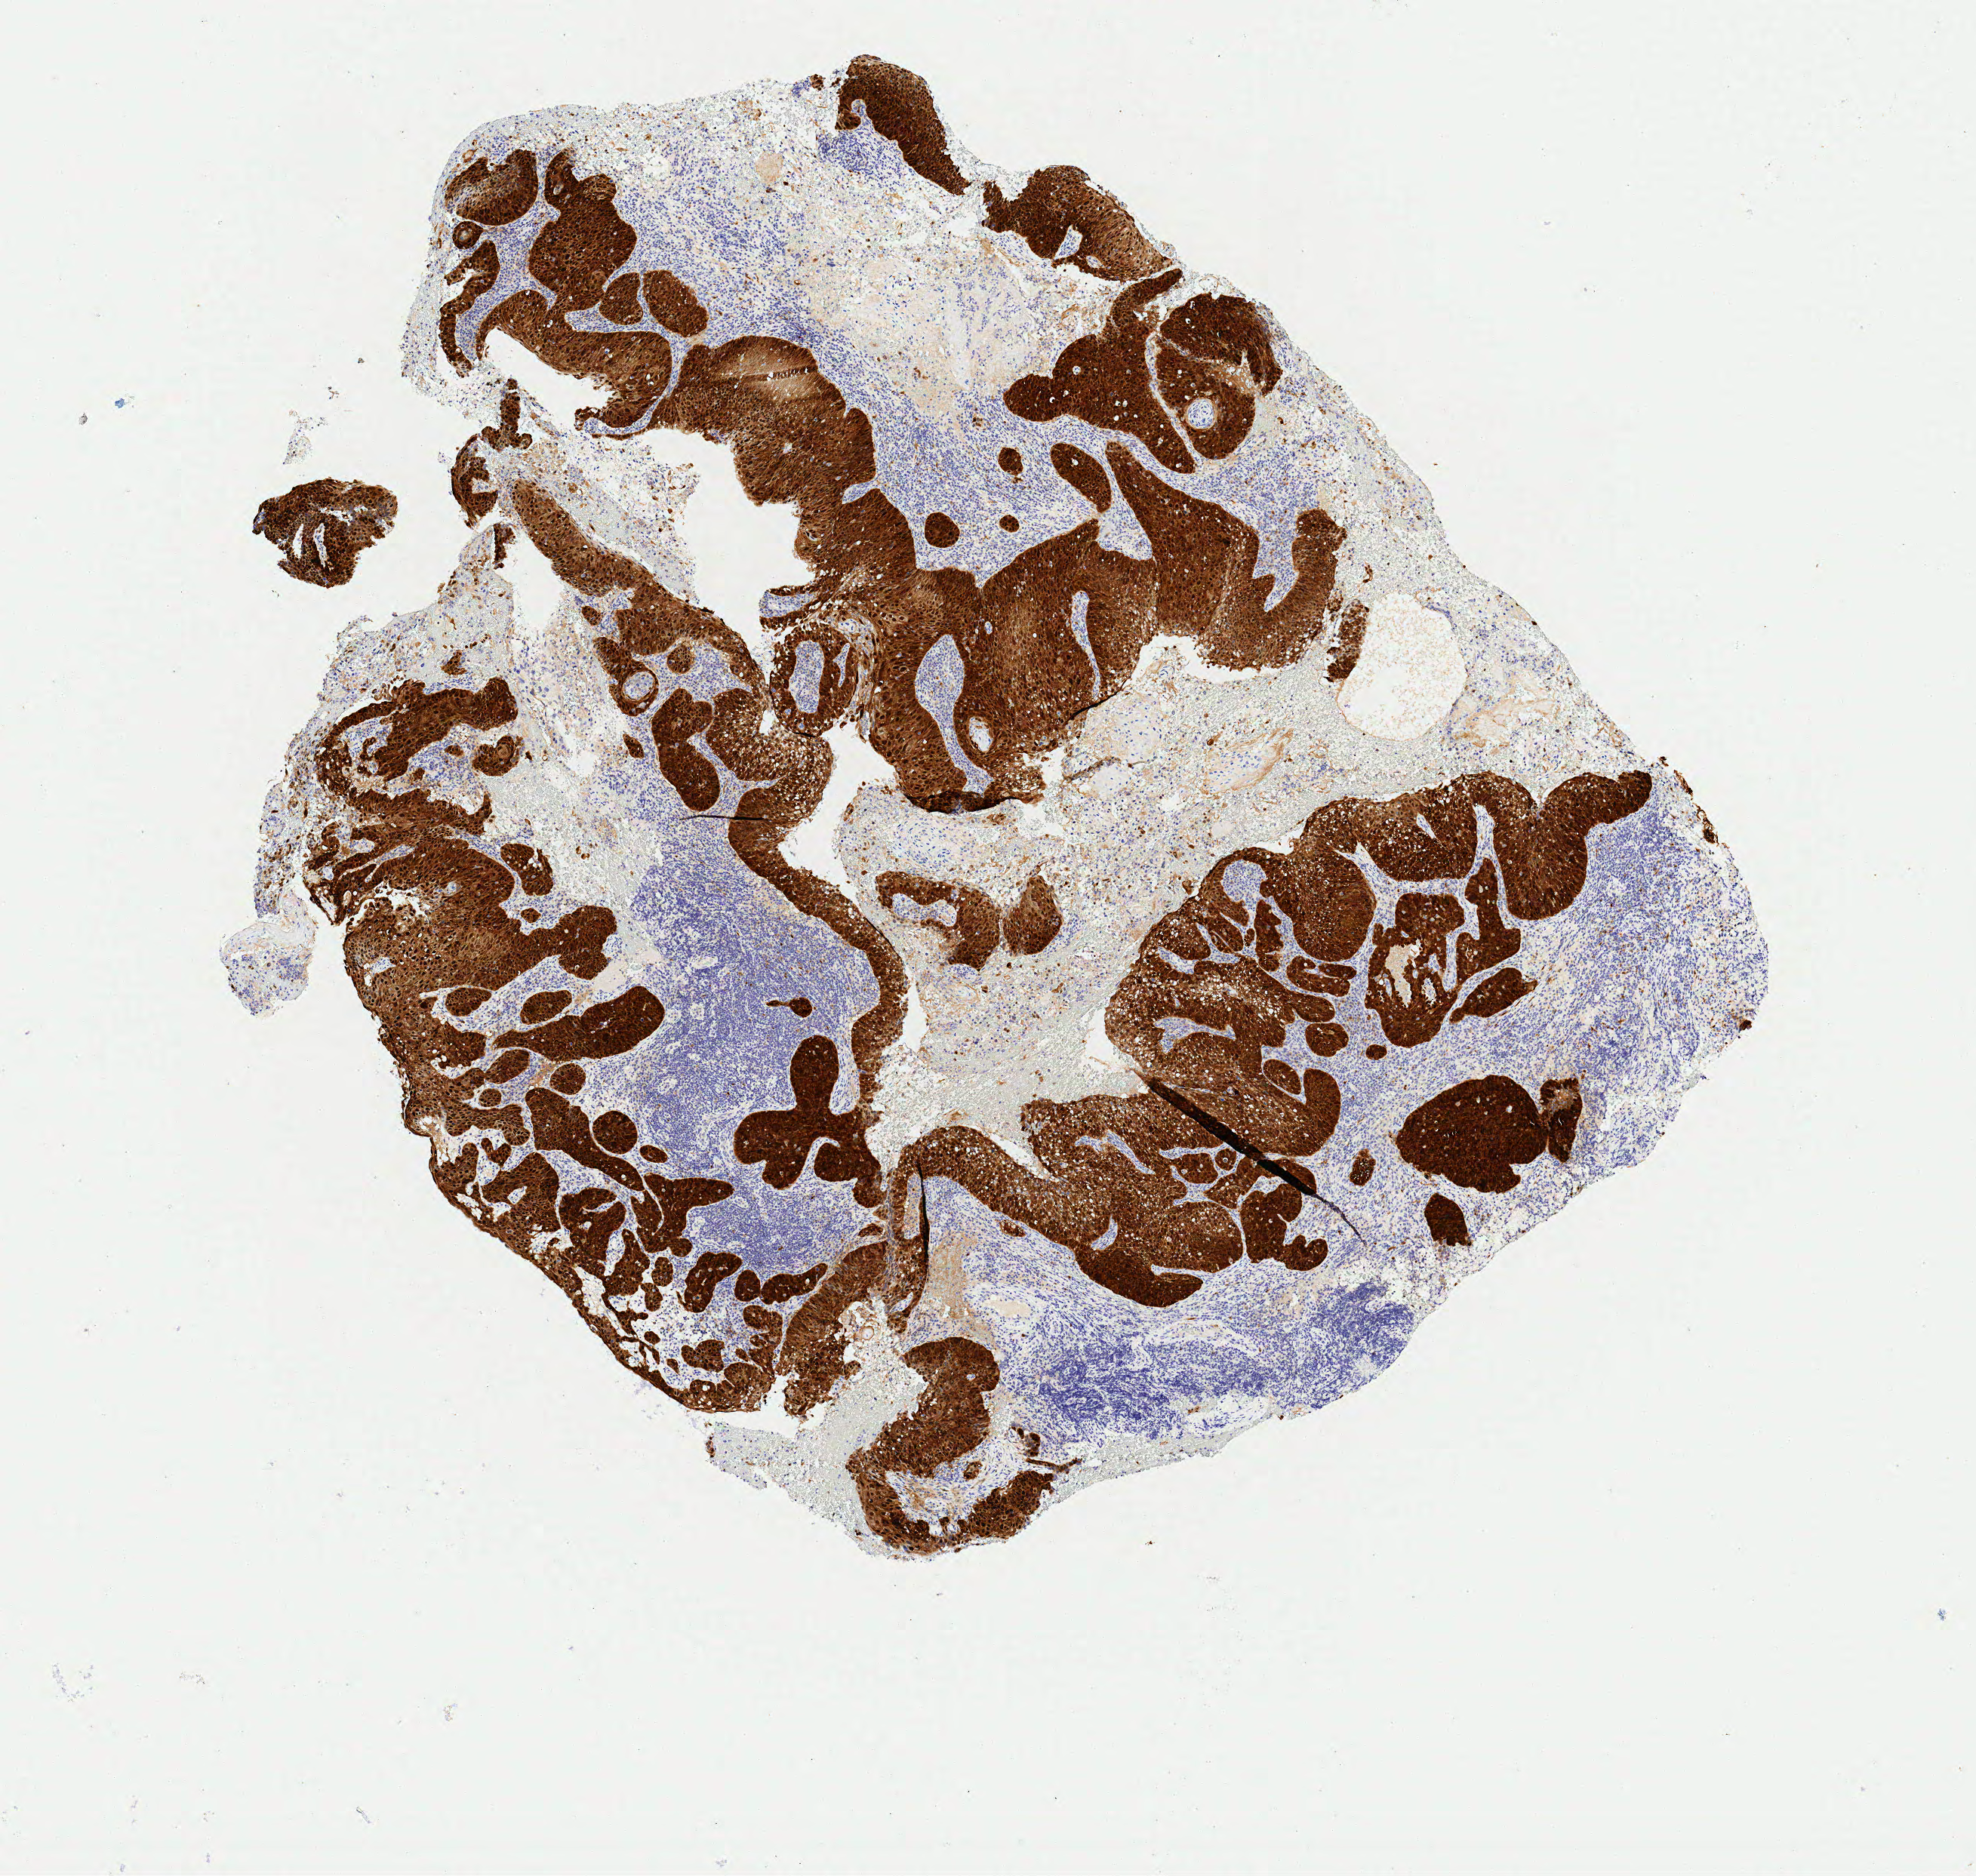
IHC for p16 (p16INK4a), whole-slide image — shown as a low-resolution overview of the whole scanned area (about 5.2 x 4.9 mm). Tumor tissue. Anatomic site: cervix. Female patient, age 60 years.
Diagnosis: Squamous cell carcinoma, keratinizing, NOS.